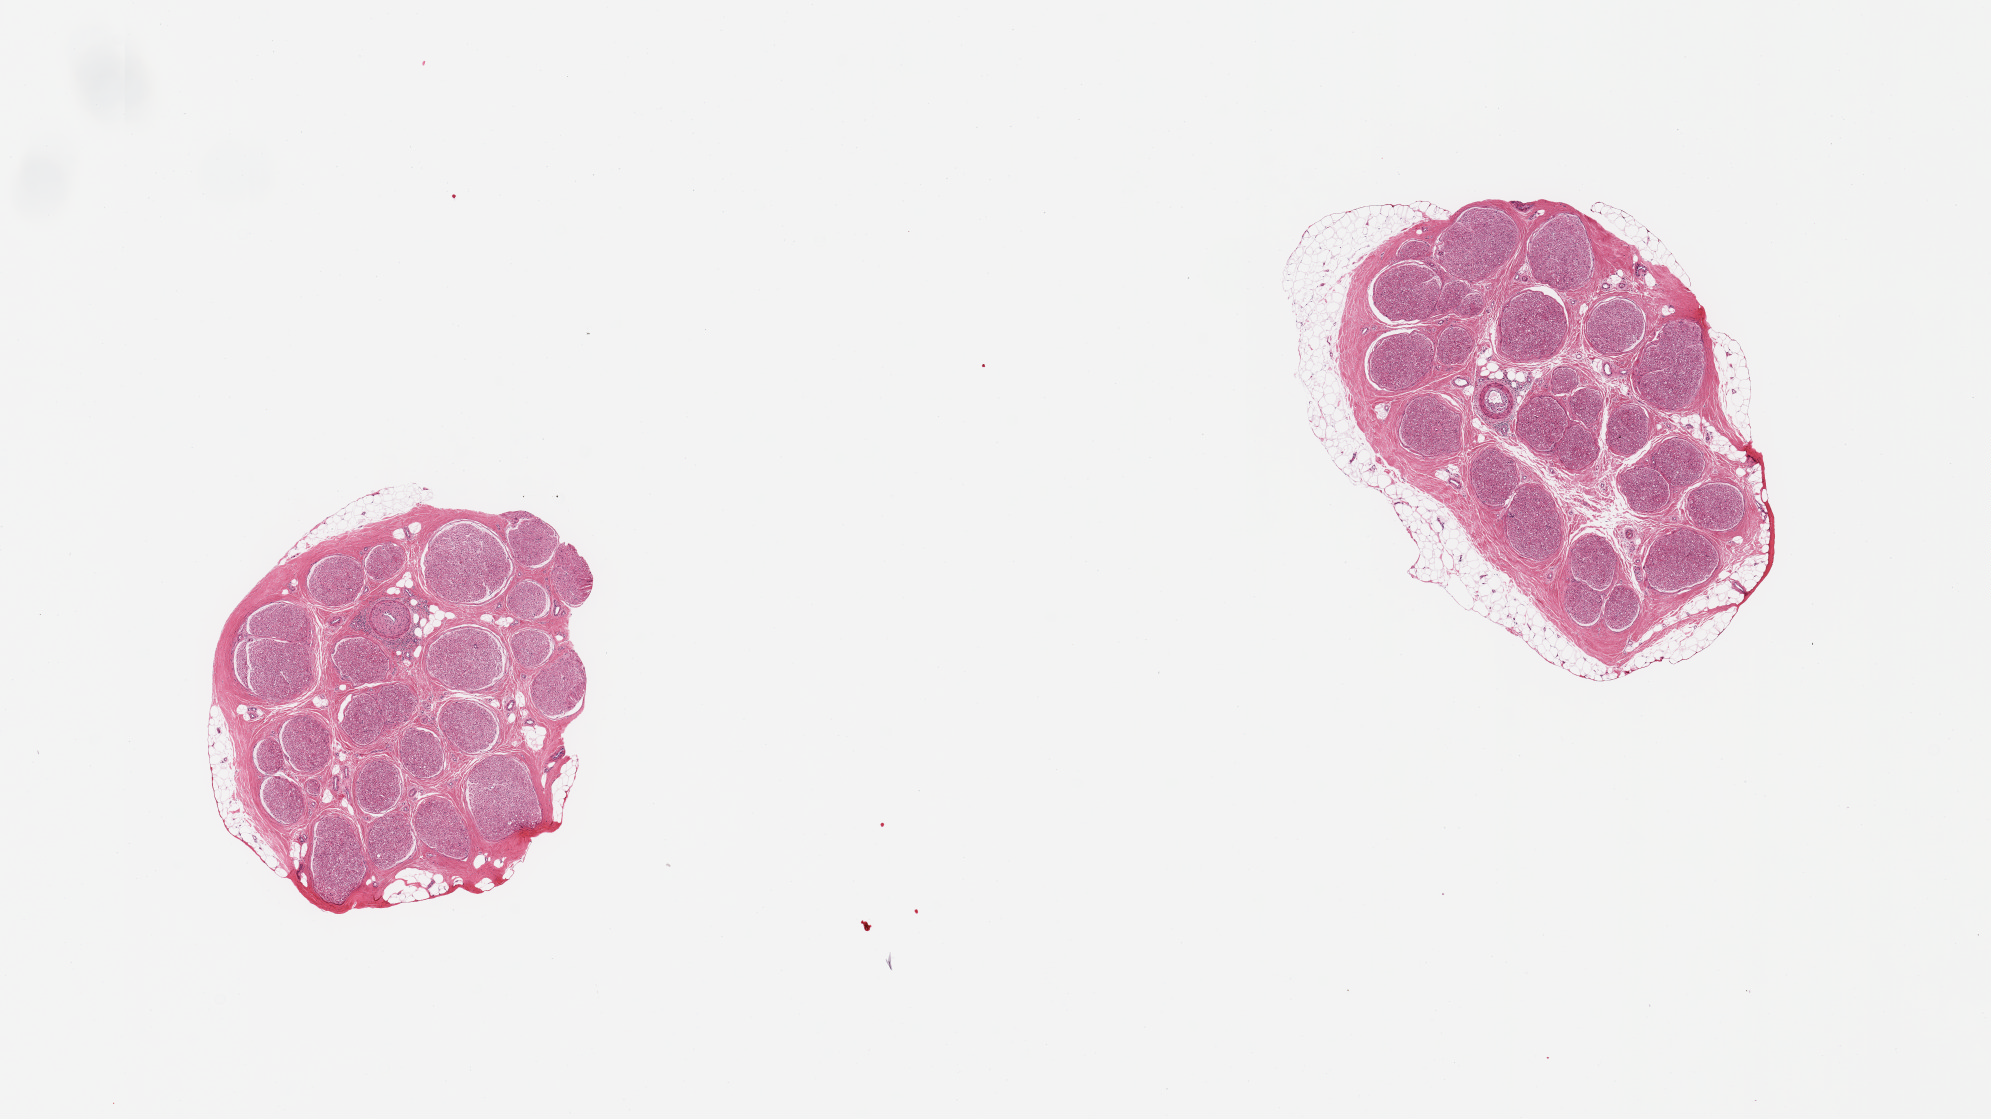
Hematoxylin and eosin (H&E) whole-slide image, shown as a low-resolution overview of the whole scanned area (about 15.8 x 8.9 mm), PAXgene-fixed paraffin-embedded (PFPE) section, section of tibial nerve (target tissue), tissue donor sample. Donor: female.
- pathologist's review note for this sample: 2 pieces, trace partial rim of adherent fat up to ~0.5mm